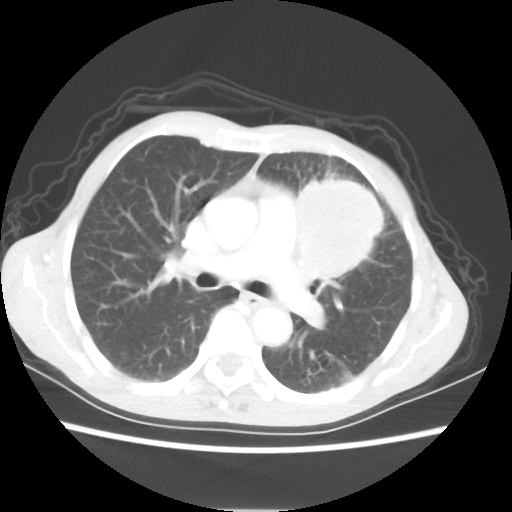
Chest CT, one axial slice; slice 36 of 56 in the series (ordered by position); reconstruction kernel STANDARD; lung window (W 1500 / L -600 HU); 512 × 512 image matrix, field of view 331 × 331 mm. Female patient, age 60 years. Case-level facts recorded for this patient, not image findings: clinical TNM (as recorded): T4 N1 M0.
Outlined on this slice (bounding box drawn by a radiologist):
- lung tumour (recorded histology: adenocarcinoma): box from (x=290, y=169) to (x=388, y=284) px